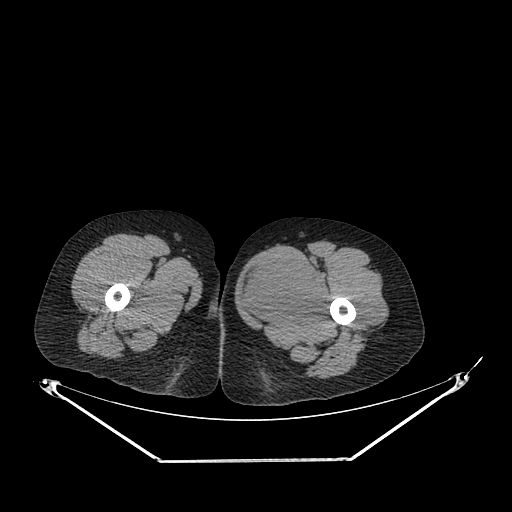
CT of an extremity soft-tissue mass (from a PET/CT study), one axial slice. Slice 244 of 267 in the series (ordered by position). Reconstruction kernel SOFT. 120 kVp. Soft-tissue window (W 400 / L 40 HU). 3.75 mm slice thickness. 512 × 512 image matrix, field of view 500 × 500 mm. Female patient. Case-level facts recorded for this patient, not image findings: histological type: pleiomorphic leiomyosarcoma; grade: intermediate; site of the primary tumour: left thigh.
Annotated regions visible in this slice (expert contour drawn on MRI and transferred to this co-registered scan by the dataset authors):
- gross tumour volume including surrounding oedema: bounding box (x1, y1, x2, y2) in pixels: (240, 258, 328, 328)
- gross tumour volume (mass): (240, 260, 328, 327)